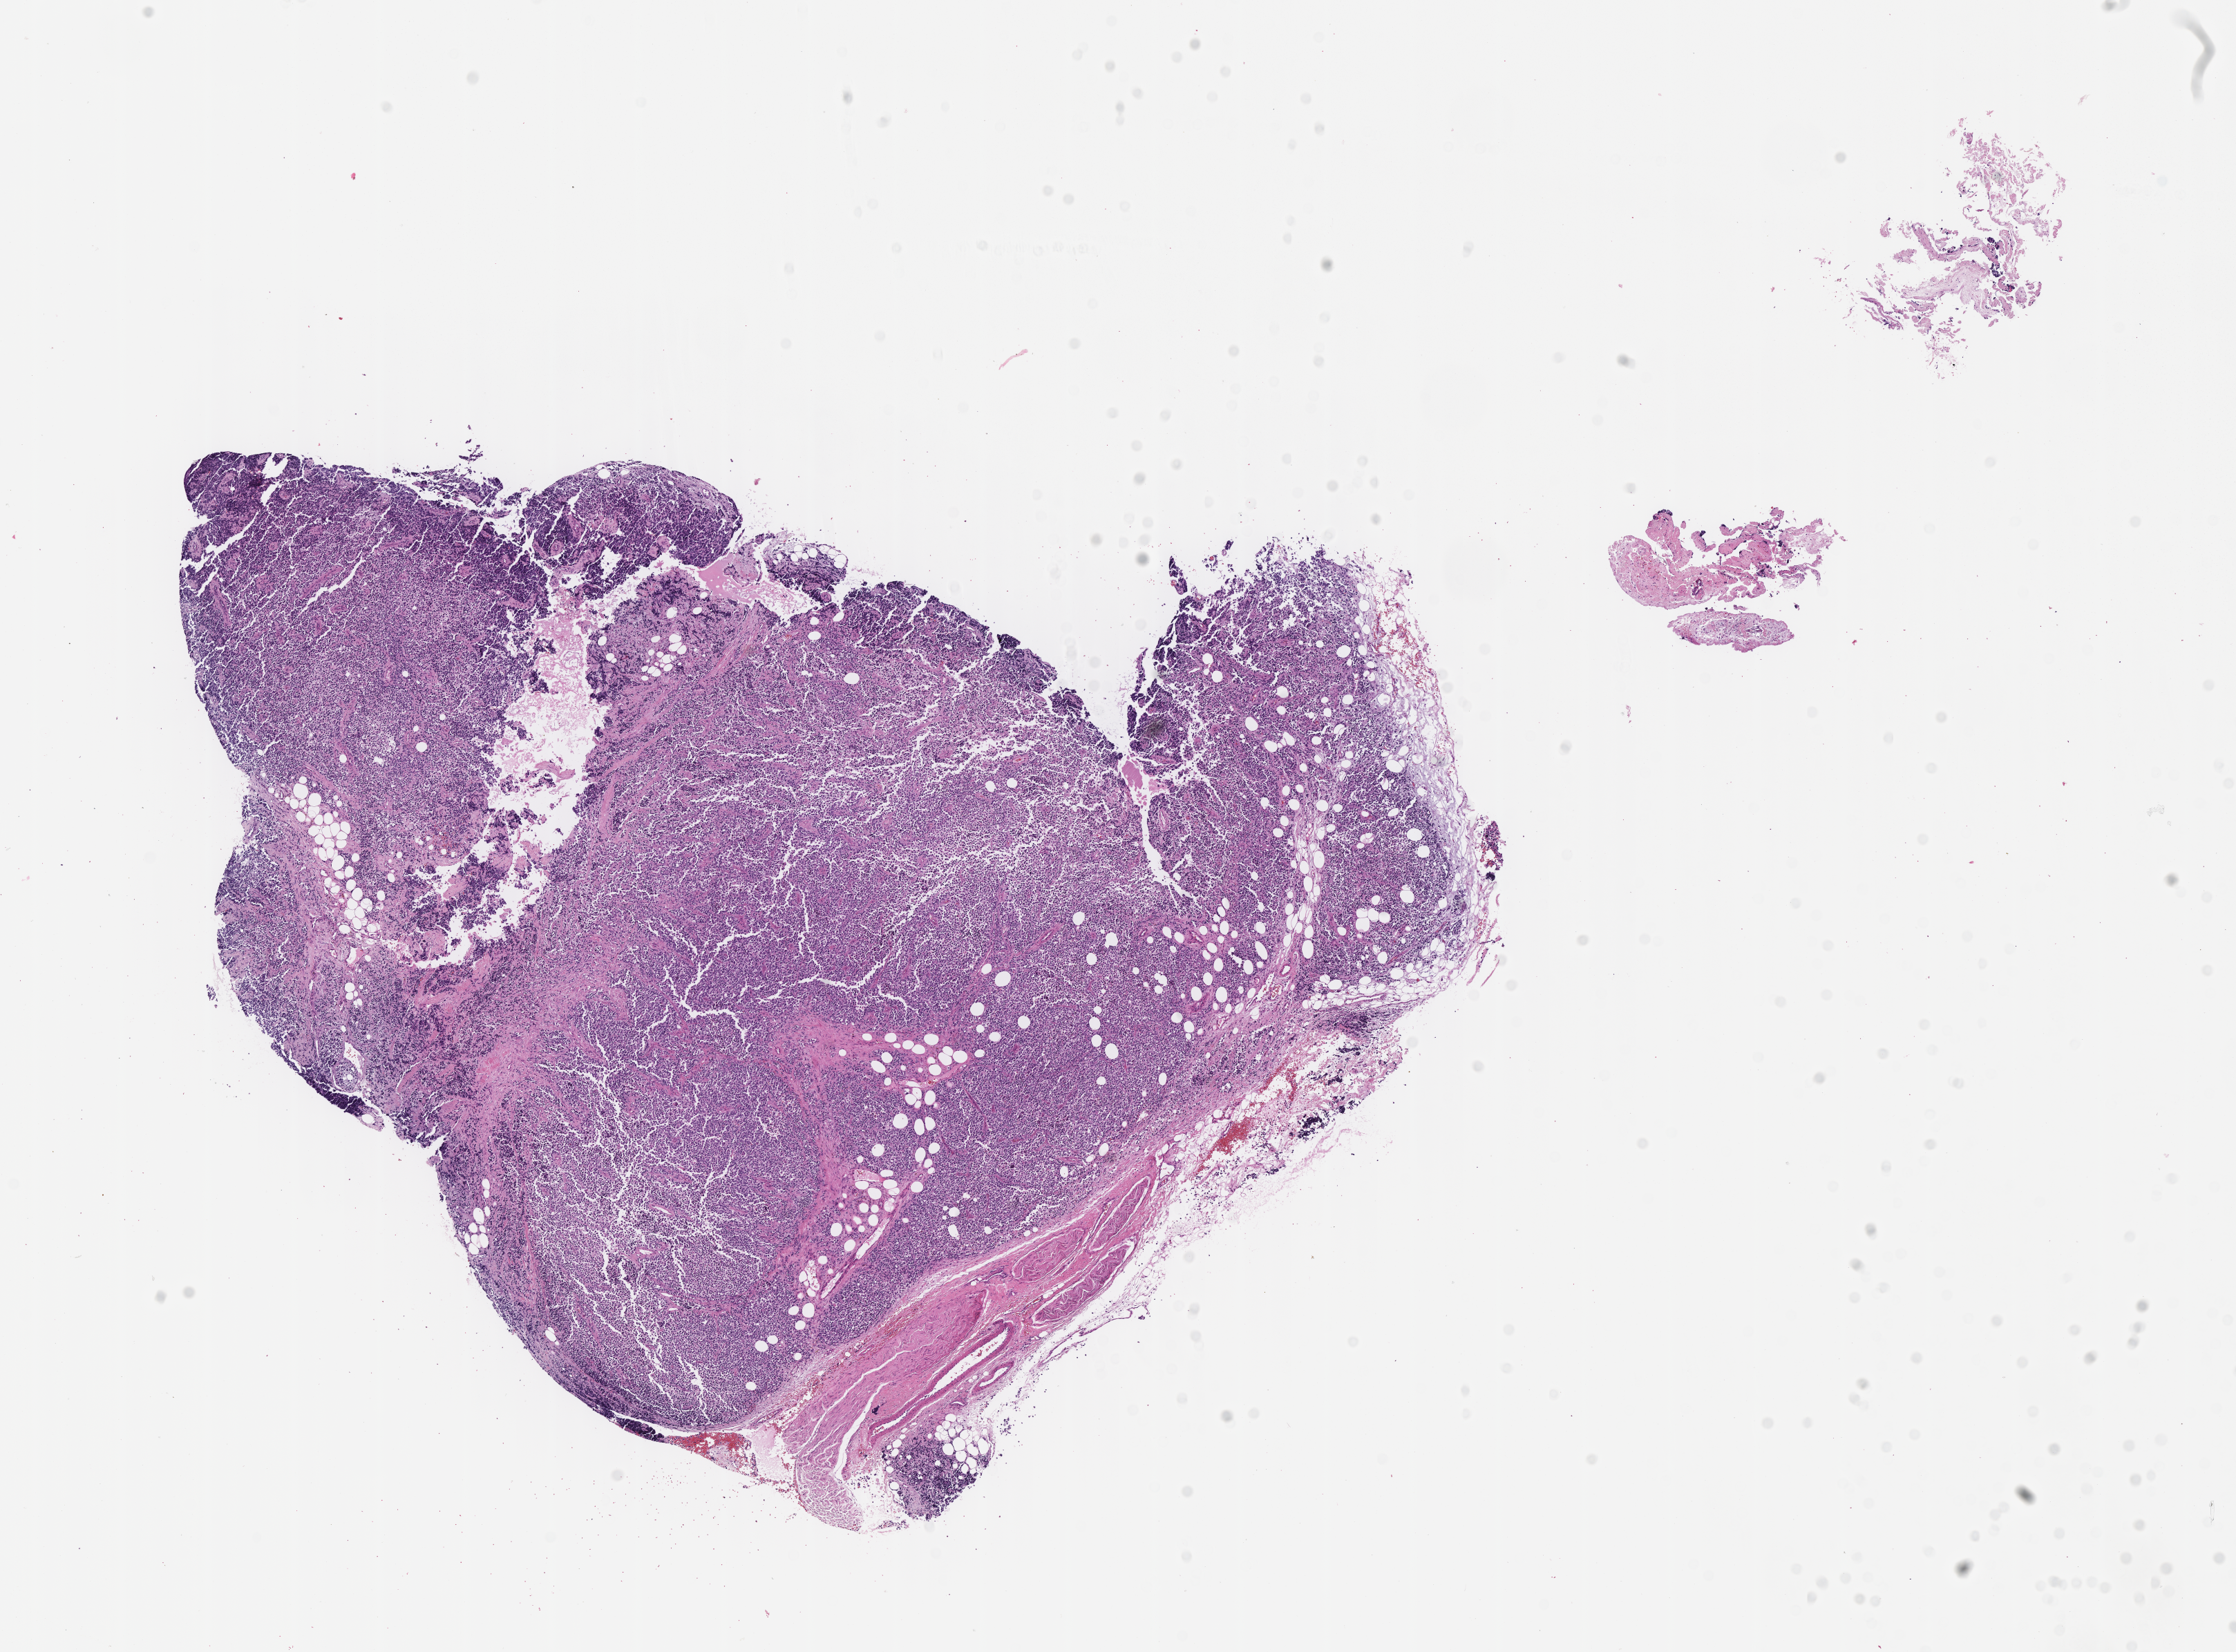
Hematoxylin and eosin (H&E) whole-slide image of tumor tissue — whole scanned area (about 13.1 x 9.7 mm) shown as a low-resolution overview; formalin-fixed, paraffin-embedded (FFPE) tissue; site: arm, left. Male patient, age at diagnosis 7.1 years.
Diagnosis: rhabdomyosarcoma; histological classification: alveolar rhabdomyosarcoma.